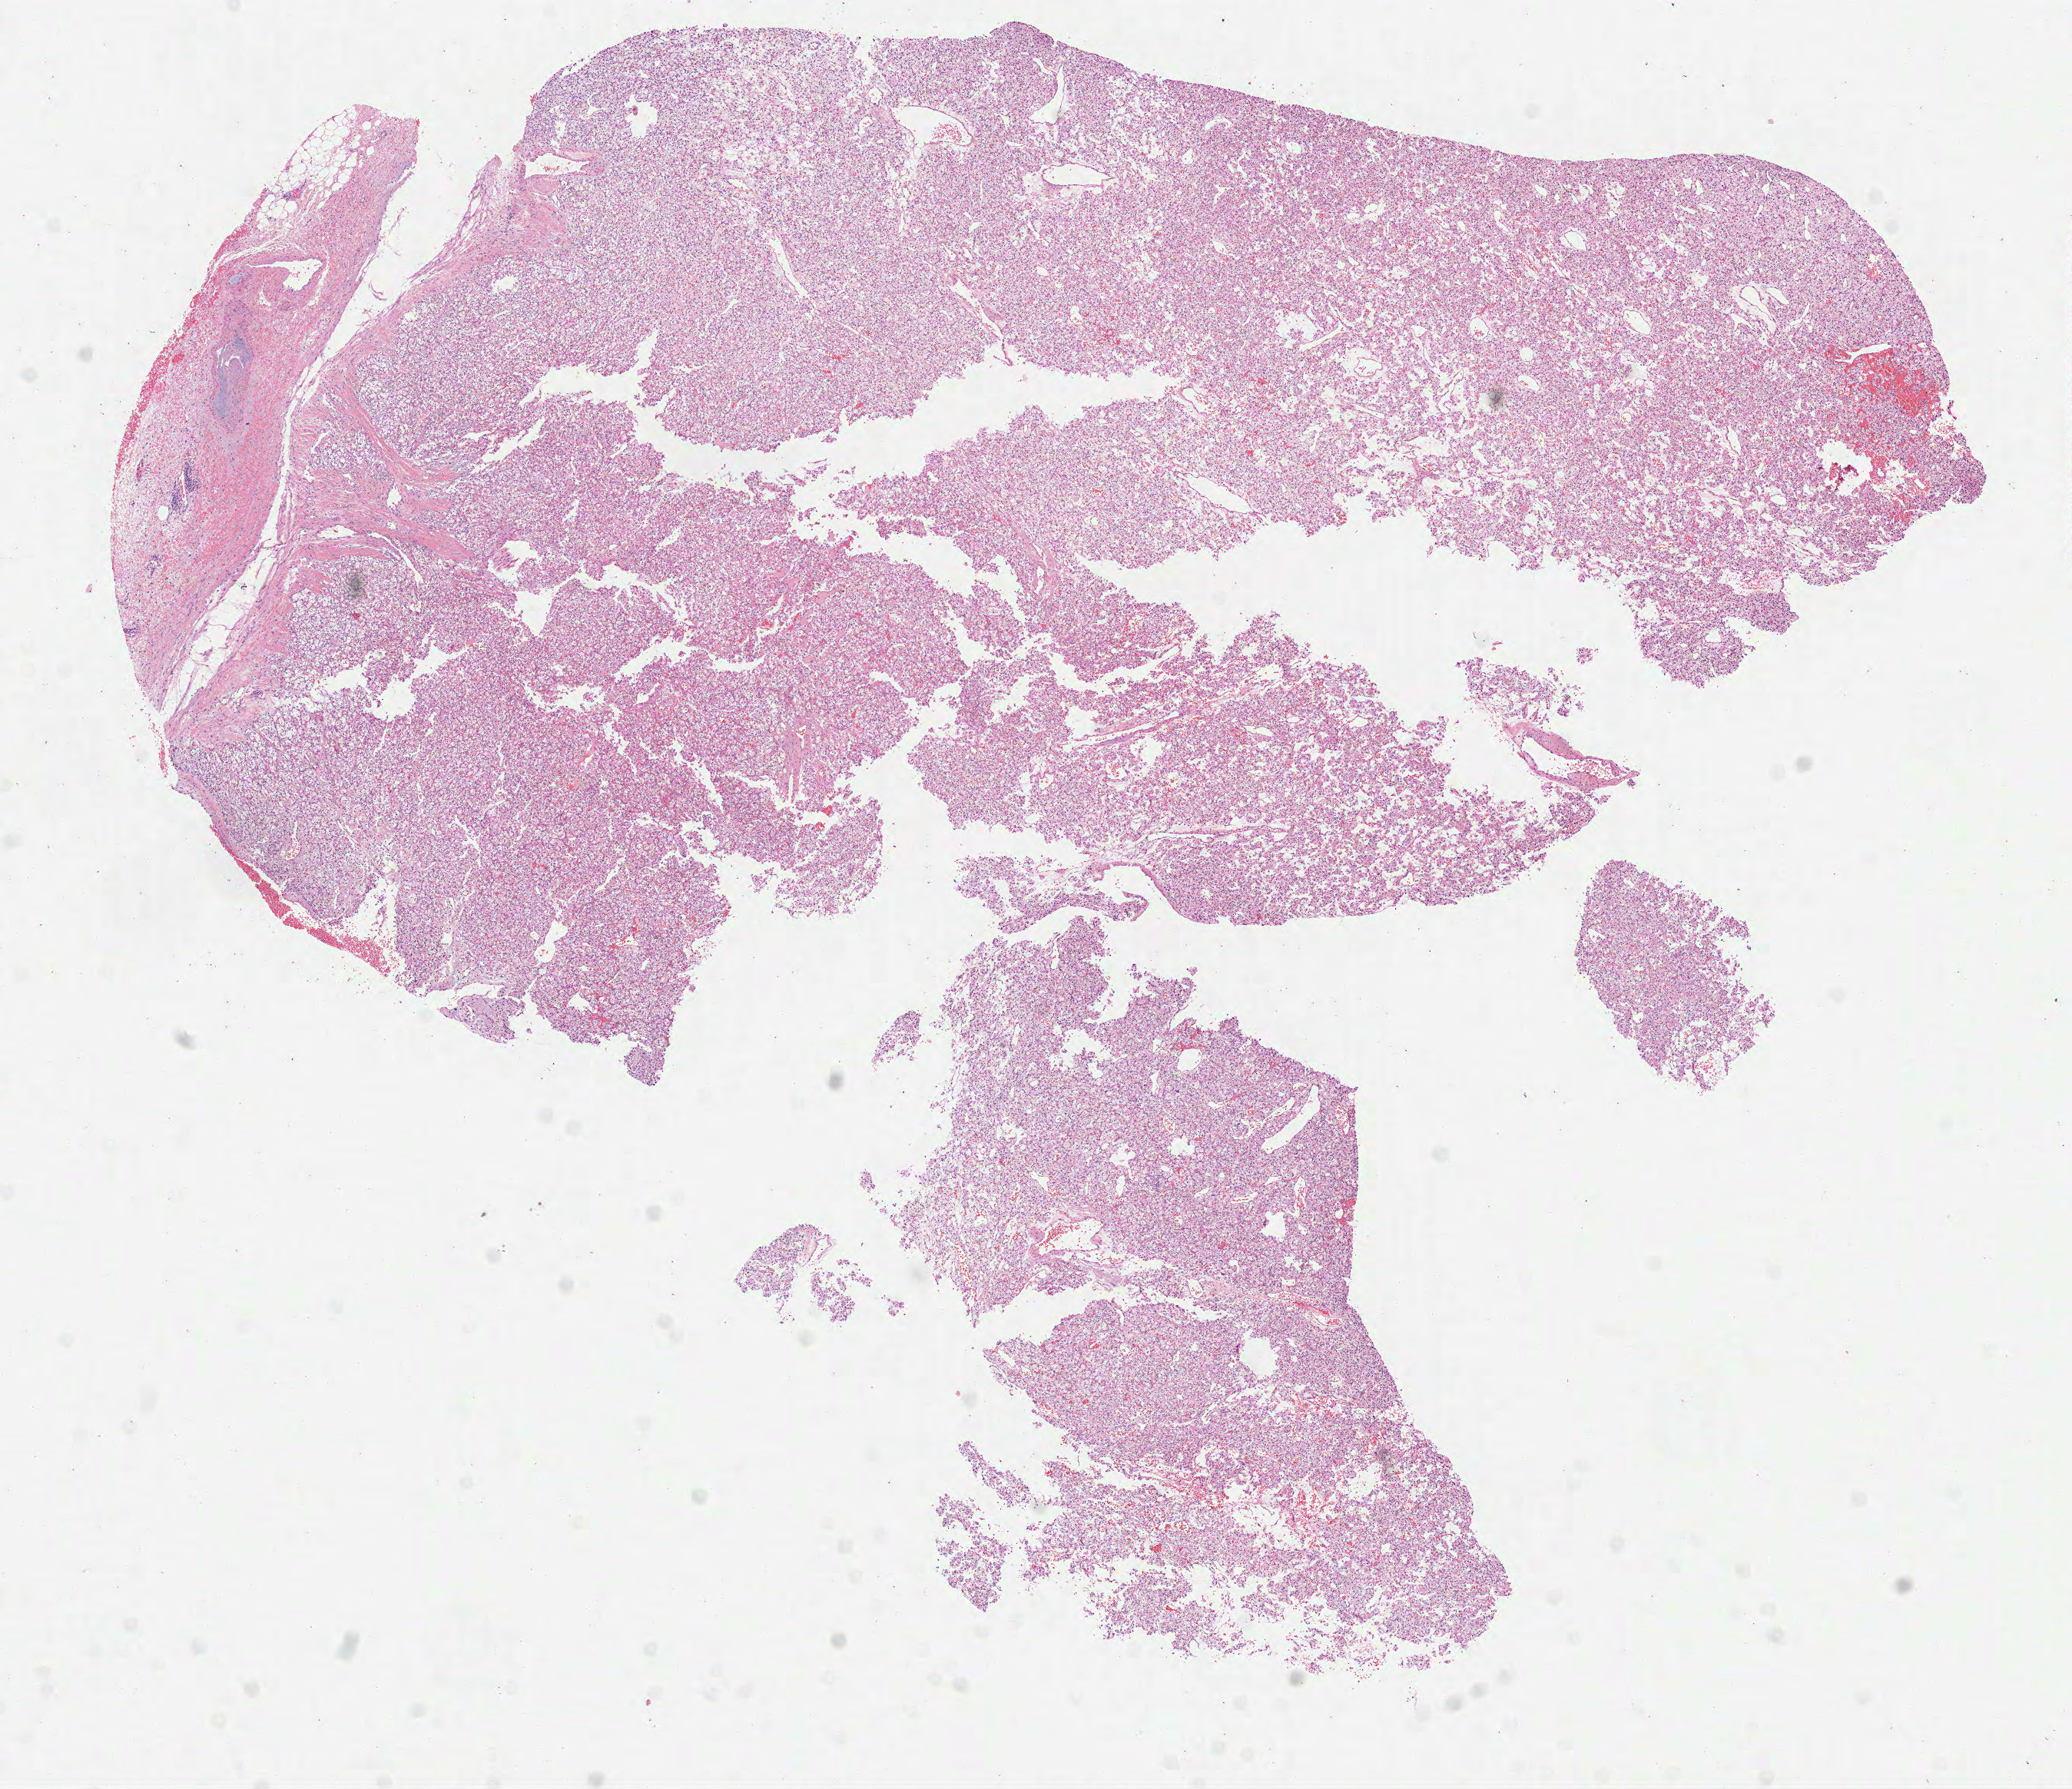
Digitized H&E-stained tissue section (whole slide) — whole scanned area (about 10.9 x 9.4 mm) shown as a low-resolution overview, FFPE section, sample: primary tumour, kidney. Female, age 60 years at initial diagnosis.
Histologic diagnosis: Clear cell adenocarcinoma, NOS.